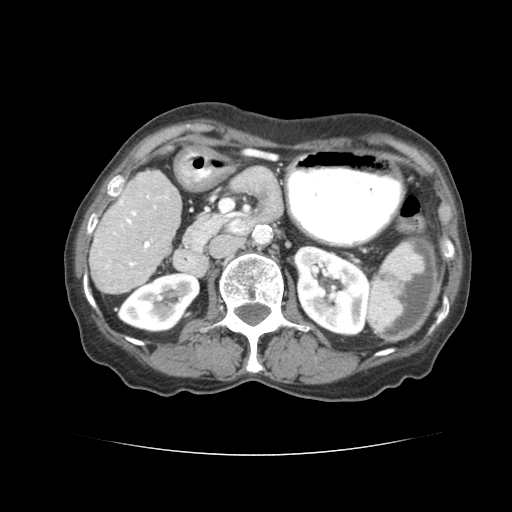
Contrast-enhanced abdominal CT (liver protocol), one axial slice; position 24 of 77 along the scan axis; reconstruction kernel STANDARD; 120 kVp; soft-tissue window (W 400 / L 40 HU); 2.5 mm slice thickness; 512 × 512 image matrix. Case-level facts recorded for this patient, not image findings: diagnosis: hepatocellular carcinoma (patient treated with transarterial chemoembolisation; whether this scan precedes or follows treatment is not stated here); TNM stage (as recorded): Stage-I; Child-Pugh class: A; tumour differentiation: well differentiated.
Annotated regions visible in this slice (semi-automatically segmented with operator editing):
- liver parenchyma outside the tumour (the mass and vessels are separate outlines, so this box may not span the whole liver): bounding box [x1, y1, x2, y2] px = [90, 170, 180, 290]
- liver vessels: [98, 186, 156, 261]